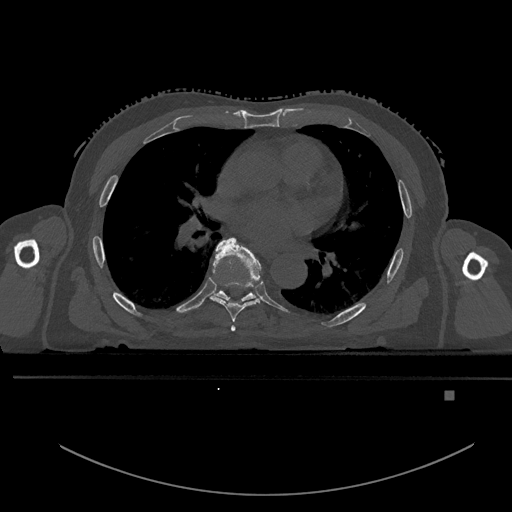
CT including the spine, one axial slice; slice 287 of 969 in the series (ordered by position); bone window (W 1800 / L 400 HU); 0.5 mm slice thickness; 512 × 512 image matrix, field of view 456 × 456 mm. Male patient, age 82 years. Case-level facts recorded for this patient, not image findings: primary cancer: prostate.
Outlined on this slice (semi-automatic segmentation, software-assisted and operator-edited):
- T5 vertebra: bounding box [x1, y1, x2, y2] px = [231, 325, 236, 331]
- T6 vertebra: [210, 237, 261, 322]
- T7 vertebra: [214, 291, 256, 301]